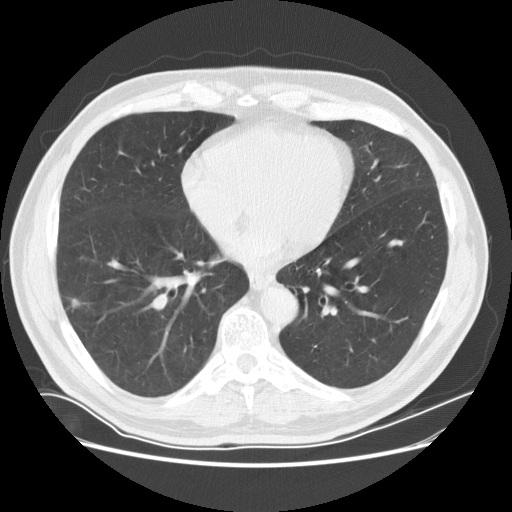
Chest CT (low-dose screening protocol), one axial image, baseline screening round, lung window (W 1500 / L -600 HU), 2.5 mm slice thickness, standard (soft-tissue) reconstruction kernel (STANDARD), slice 98 of 170 in the series, 512 × 512 image matrix. Male participant, aged 72 years at enrolment. Current smoker at enrolment.
Expert reader's lesion annotation, box from (x=54, y=290) to (x=90, y=322) px. Reader record for this screening exam (exam-level; its link to the box is not recorded): non-calcified nodule or mass ≥4 mm, right lower lobe, 13 × 8 mm, poorly defined margins, soft tissue attenuation. Official screen result: positive, change unspecified: nodule(s) >= 4 mm or enlarging nodule(s), mass(es), or other non-specific abnormalities suspicious for lung cancer. Participant outcome: lung cancer diagnosed 17 days after this screen — non-small cell carcinoma, right lower lobe, moderately differentiated (G2), stage IA (AJCC 6th edition), 10 mm at pathology.